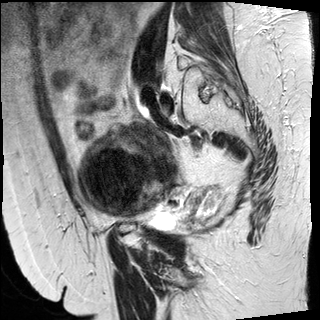
Pelvic MRI for cervical cancer, one sagittal slice. Slice 18 of 50 in the series (ordered by position). T2-weighted. 1.5 T. TE 89 ms, TR 4880 ms. 4 mm slice thickness. 320 × 320 image matrix, field of view 260 × 260 mm. Female patient, age 50 years.
Structures marked on this image (expert manual segmentation):
- uterus and cervix: box from (x=78, y=120) to (x=227, y=216) px